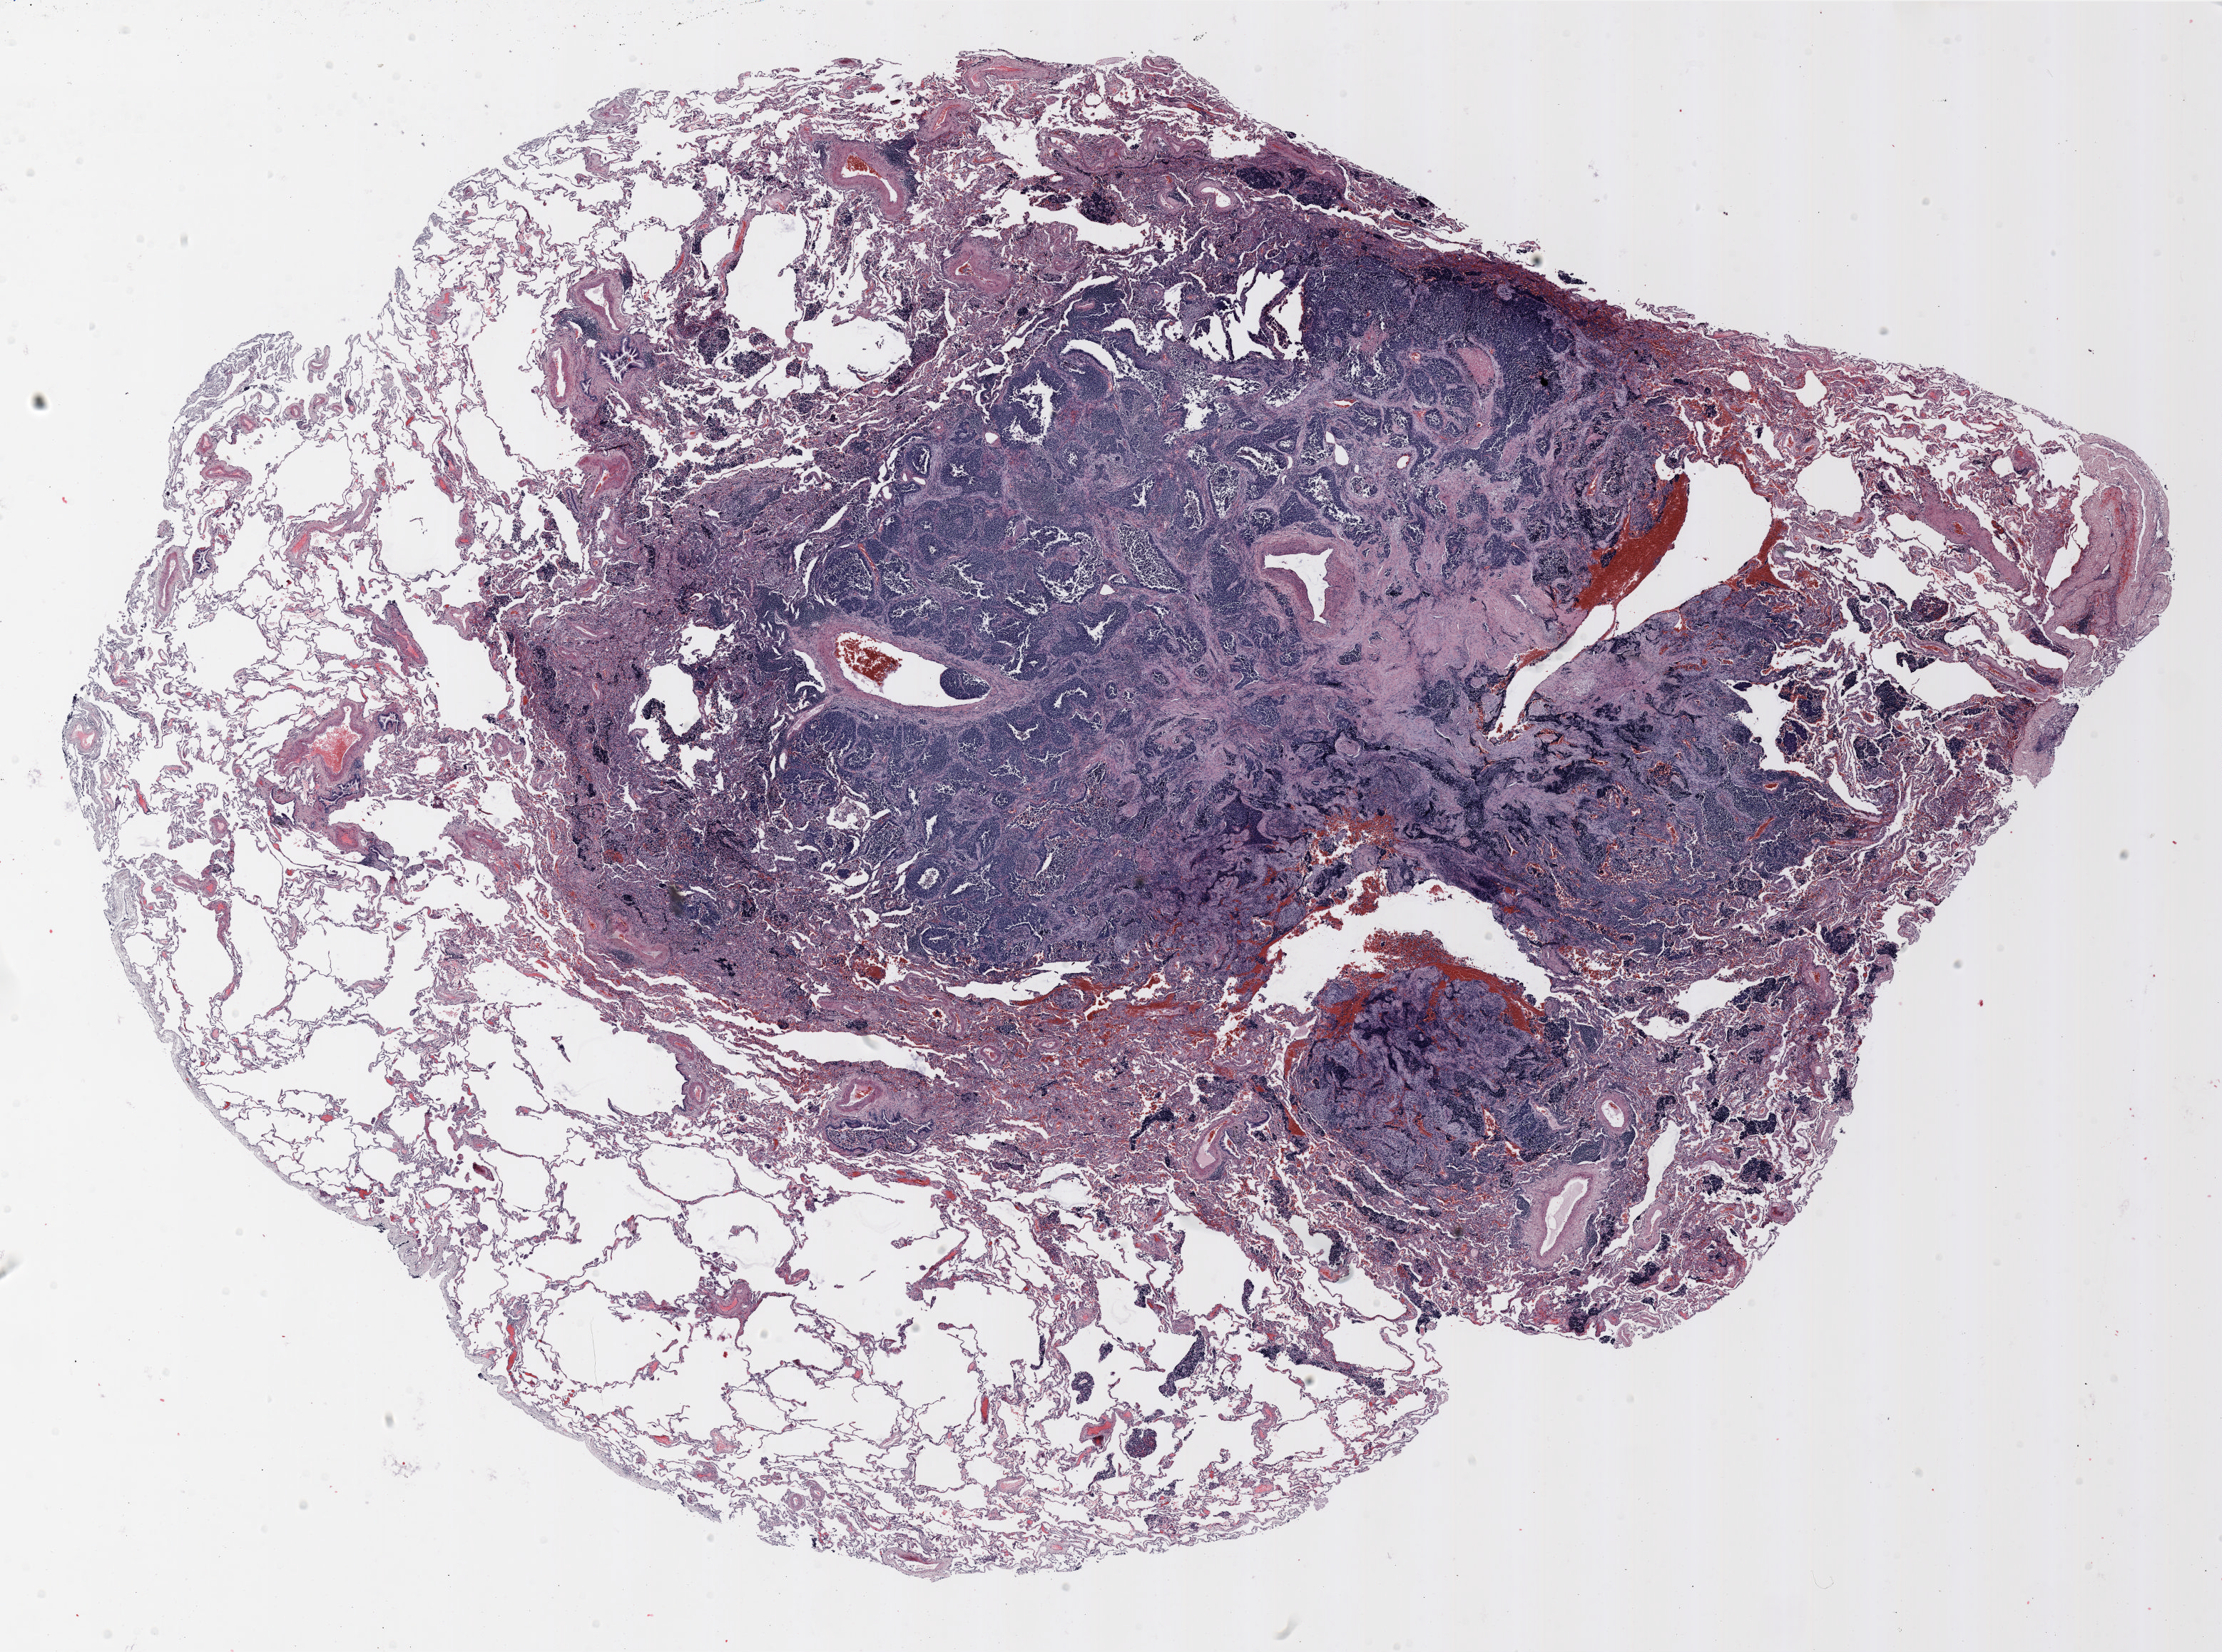
Whole-slide histology image, H&E-stained — shown as a low-resolution overview of the whole scanned area (about 25.0 x 18.6 mm, from a 20x scan), FFPE section, lung tissue. Female, age 71 at enrolment. Grade: poorly differentiated (G3).
- participant's lung-cancer diagnosis: Large cell carcinoma, NOS
- primary tumour location (clinical record): left upper lobe
- stage (AJCC 6th edition): IA
- tumour size (pathology): 13 mm